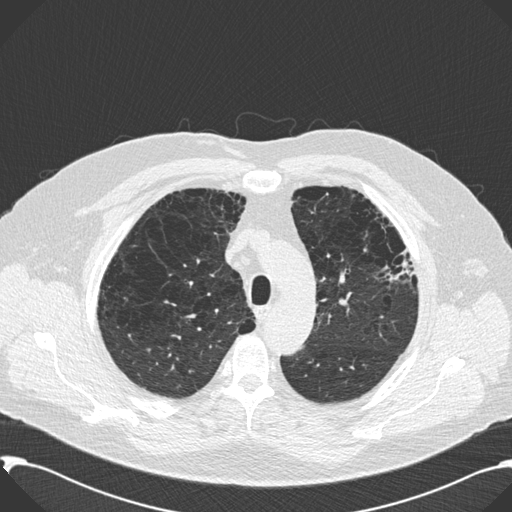
Low-dose screening chest CT, axial slice. Second annual screen. Lung window (W 1500 / L -600 HU). 2 mm slice thickness. Standard (soft-tissue) reconstruction kernel (B30f). 512 × 512 image matrix, field of view 380 × 380 mm. Male participant, aged 59 years at enrolment. Current smoker at enrolment.
Expert-annotated lung lesion, bounding box <364,220,418,299> (left, top, right, bottom; pixels). Screening reader's record for this exam: no non-calcified nodule ≥4 mm recorded. Participant outcome: lung cancer diagnosed 518 days after this screen — bronchiolo-alveolar carcinoma, mixed mucinous and non-mucinous, left upper lobe, stage IA (AJCC 6th edition), 20 mm at pathology.